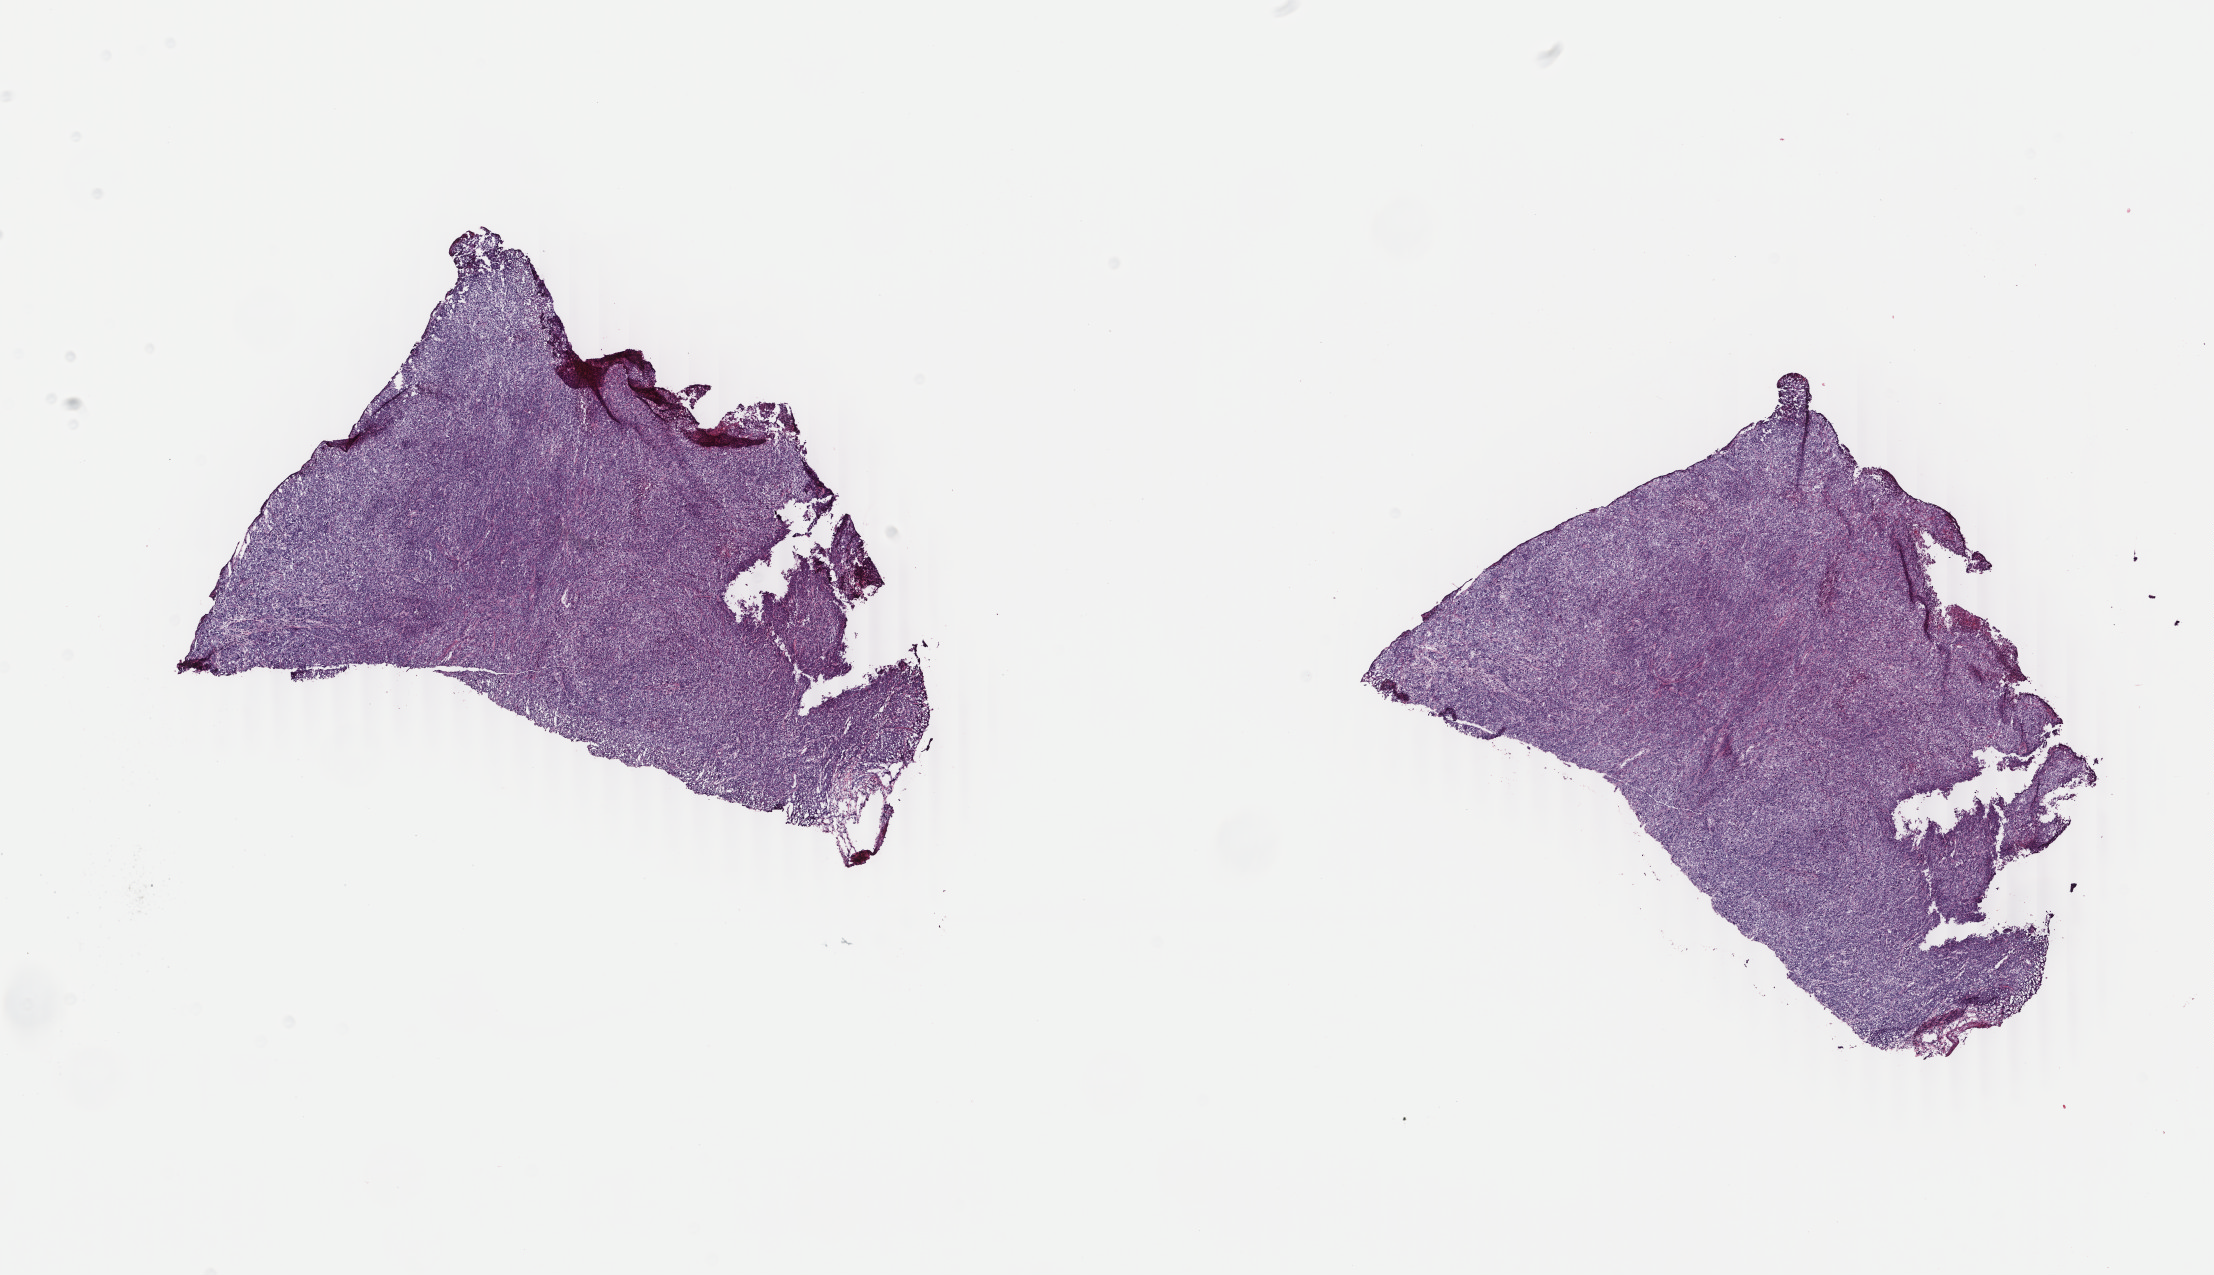
Hematoxylin and eosin (H&E) stained whole-slide image, shown as a low-resolution overview of the whole scanned area (about 17.6 x 10.1 mm, slide scanned at 40x), frozen section, cervix, primary tumour sample. Female, age 21 years at initial diagnosis. Histologic grade: G3 (poorly differentiated). Pathologist review of this section (percent, as recorded): tumour cells 90%, tumour nuclei 90%, normal cells 0%, stromal cells 5%, necrosis 5%. Inflammatory infiltration, as recorded: lymphocyte infiltration 30%, monocyte infiltration 10%, neutrophil infiltration 20%.
Histologic diagnosis: Squamous cell carcinoma, keratinizing, NOS (cervix uteri). FIGO stage: IB2.